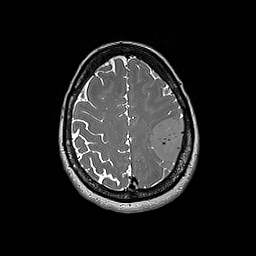
Brain MRI from a brain-tumour surgery series, one axial slice; position 60 of 192 along the scan axis; 1 mm slice thickness; 256 × 256 image matrix, field of view 250 × 250 mm. Case-level facts recorded for this patient, not image findings: histopathology: Glioblastoma; WHO grade: 4; IDH mutation: no; tumour location: Left Frontal.
Outlined on this slice (expert manual segmentation):
- tumour: box from (x=150, y=114) to (x=185, y=164) px